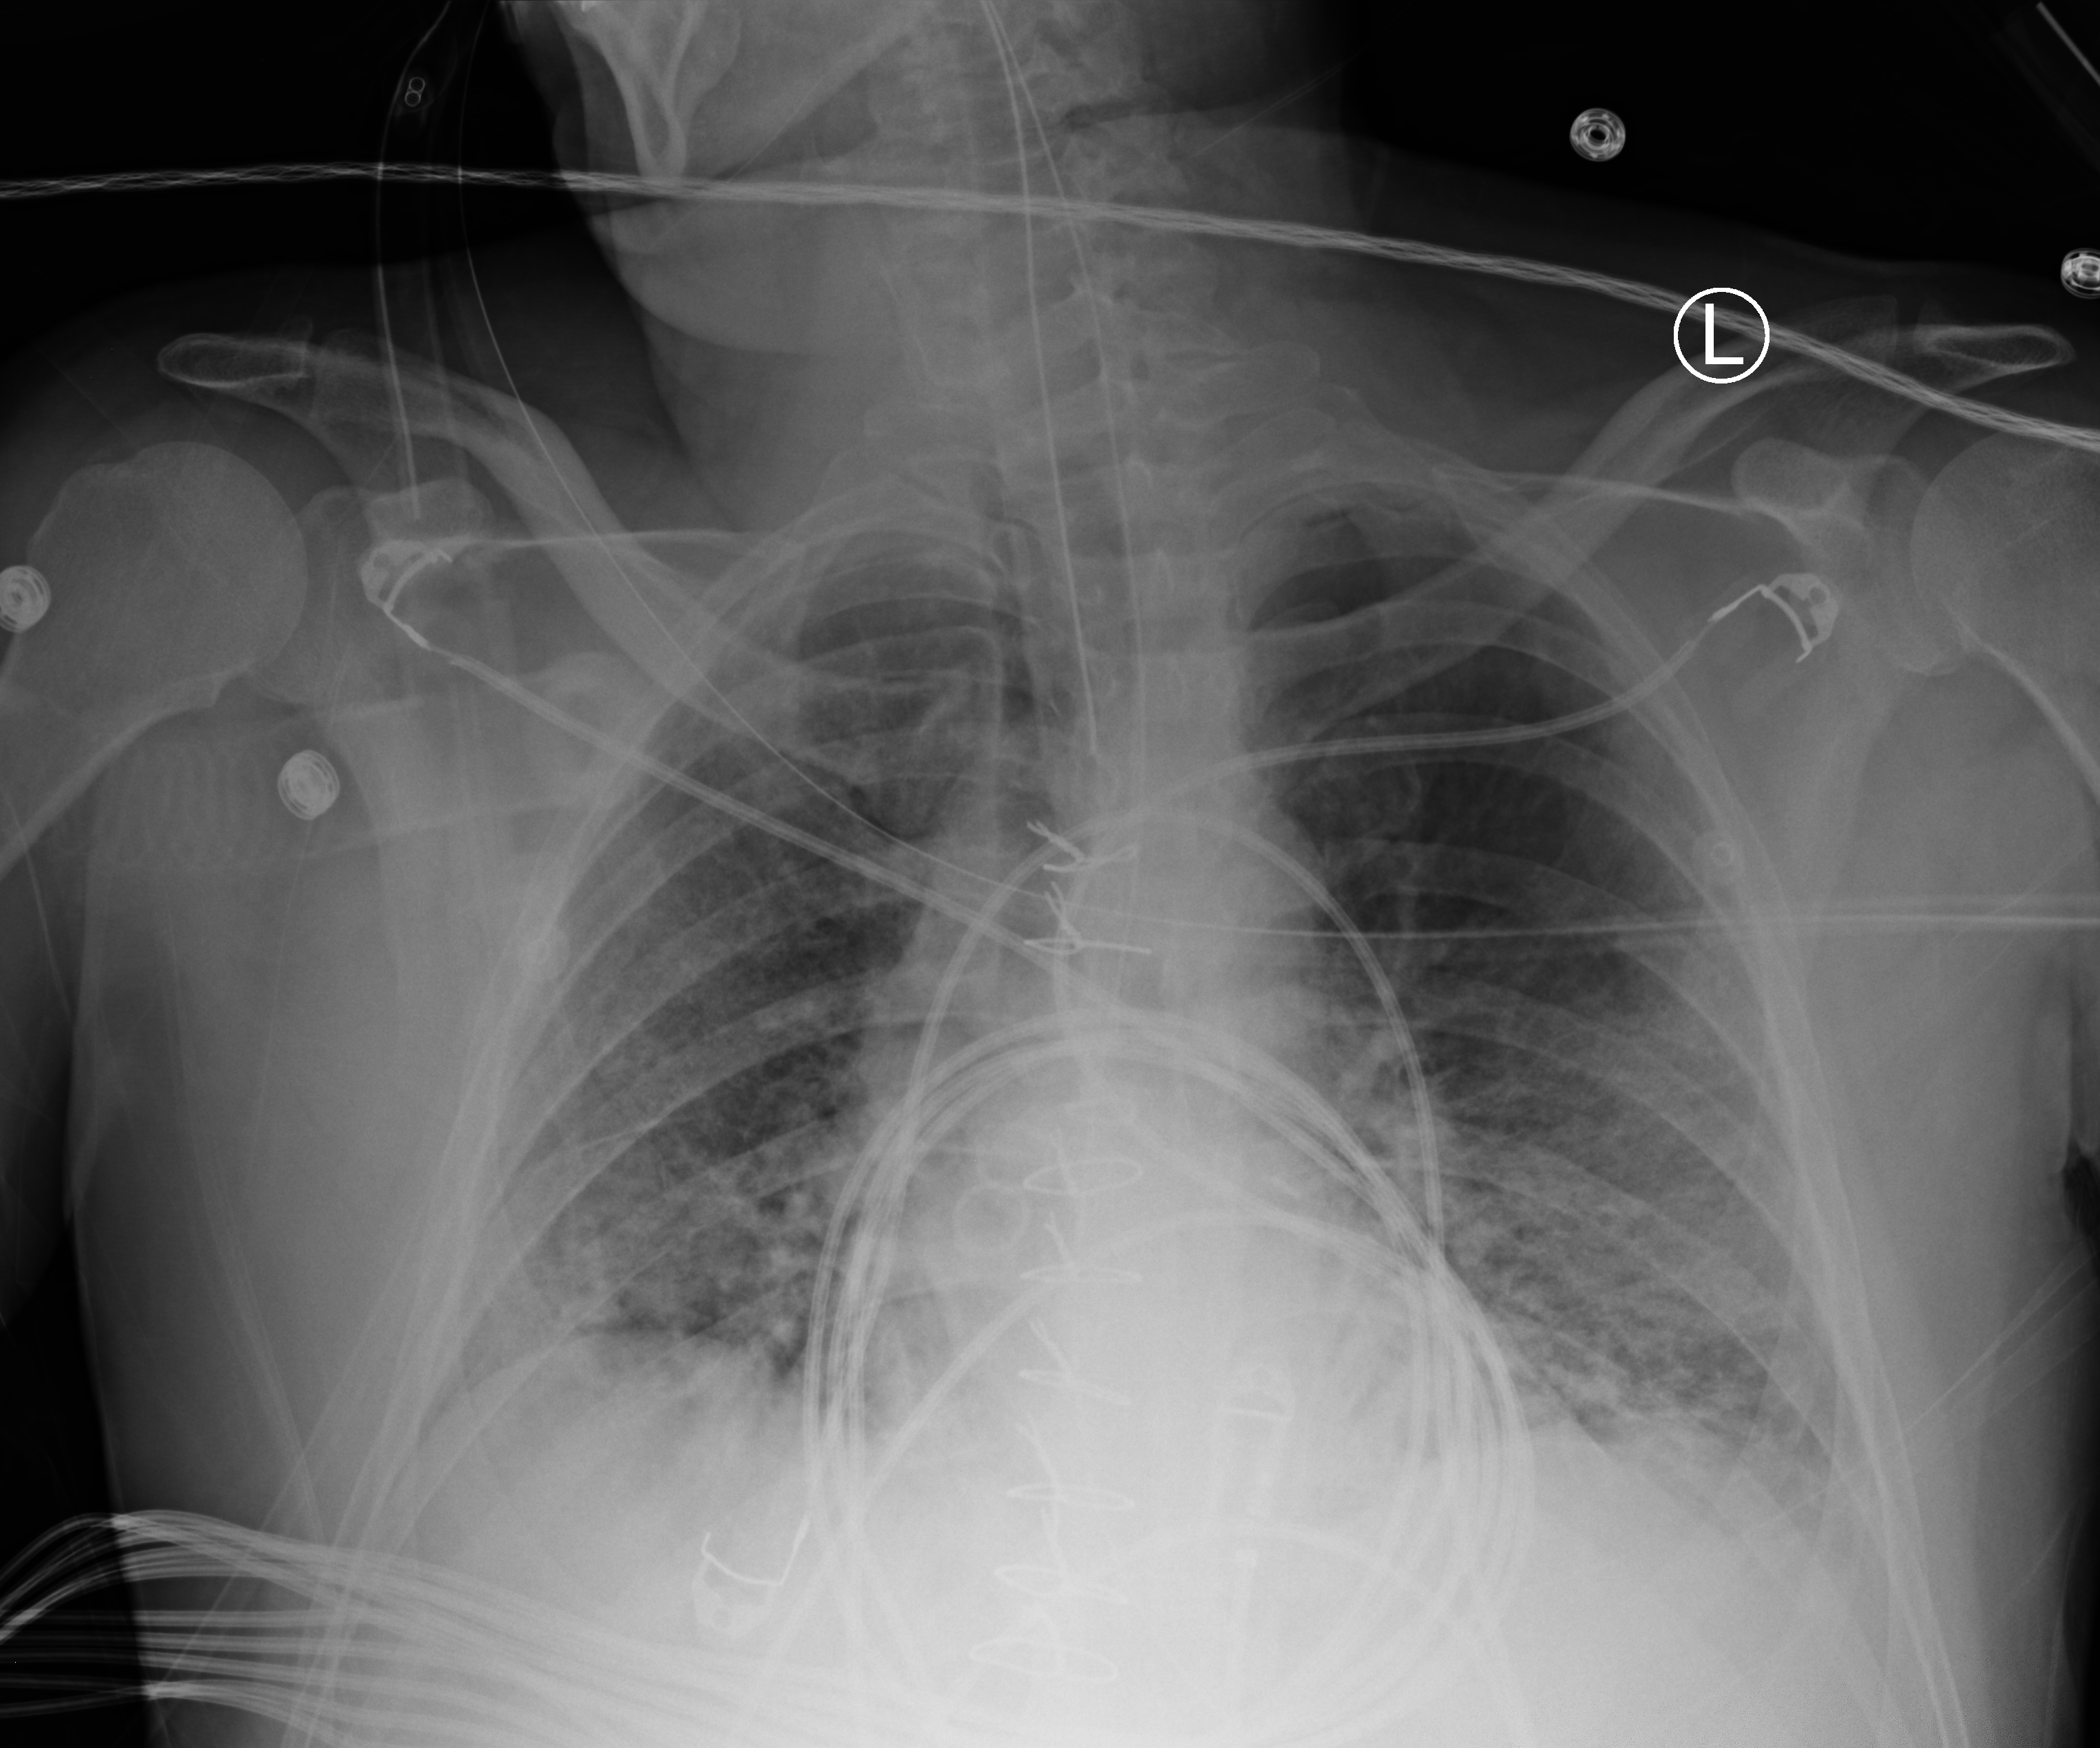
Bedside chest radiograph (computed radiography). Patient hospitalised with COVID-19; male, aged 18–59 years.
Admission-level facts for this patient (not findings on this image; timing relative to this image not recorded):
- admitted to intensive care during this hospital stay: yes
- diabetes (admission record): yes
- mechanically ventilated during this hospital stay: yes